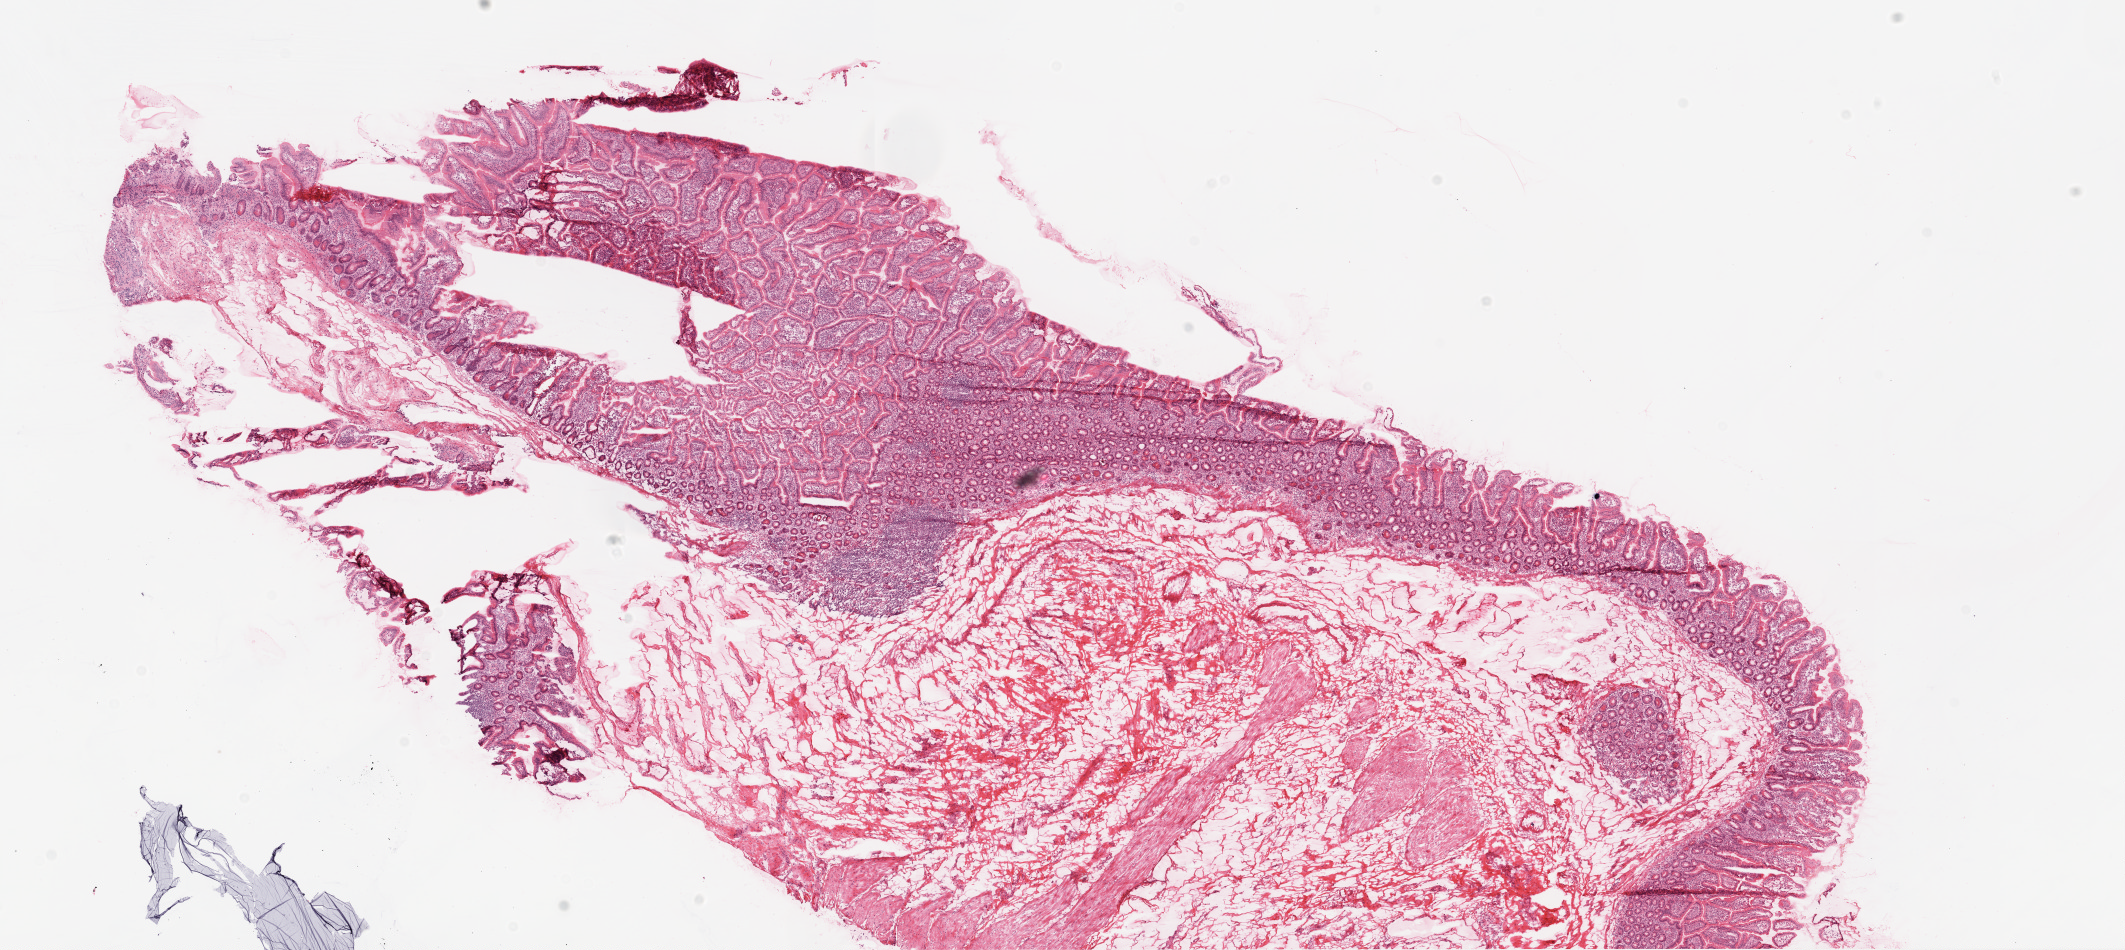
Whole-slide histology image, H&E — whole scanned area (about 17.1 x 7.6 mm, acquisition: 20x scan) shown as a low-resolution overview. Frozen section from the top of the tissue portion. Ovary, solid tissue normal (non-tumour tissue) sample. Female patient; age at initial diagnosis 40 years.
This section: solid tissue normal (non-tumour) sample from the same patient. Patient diagnosis: Serous cystadenocarcinoma, NOS.